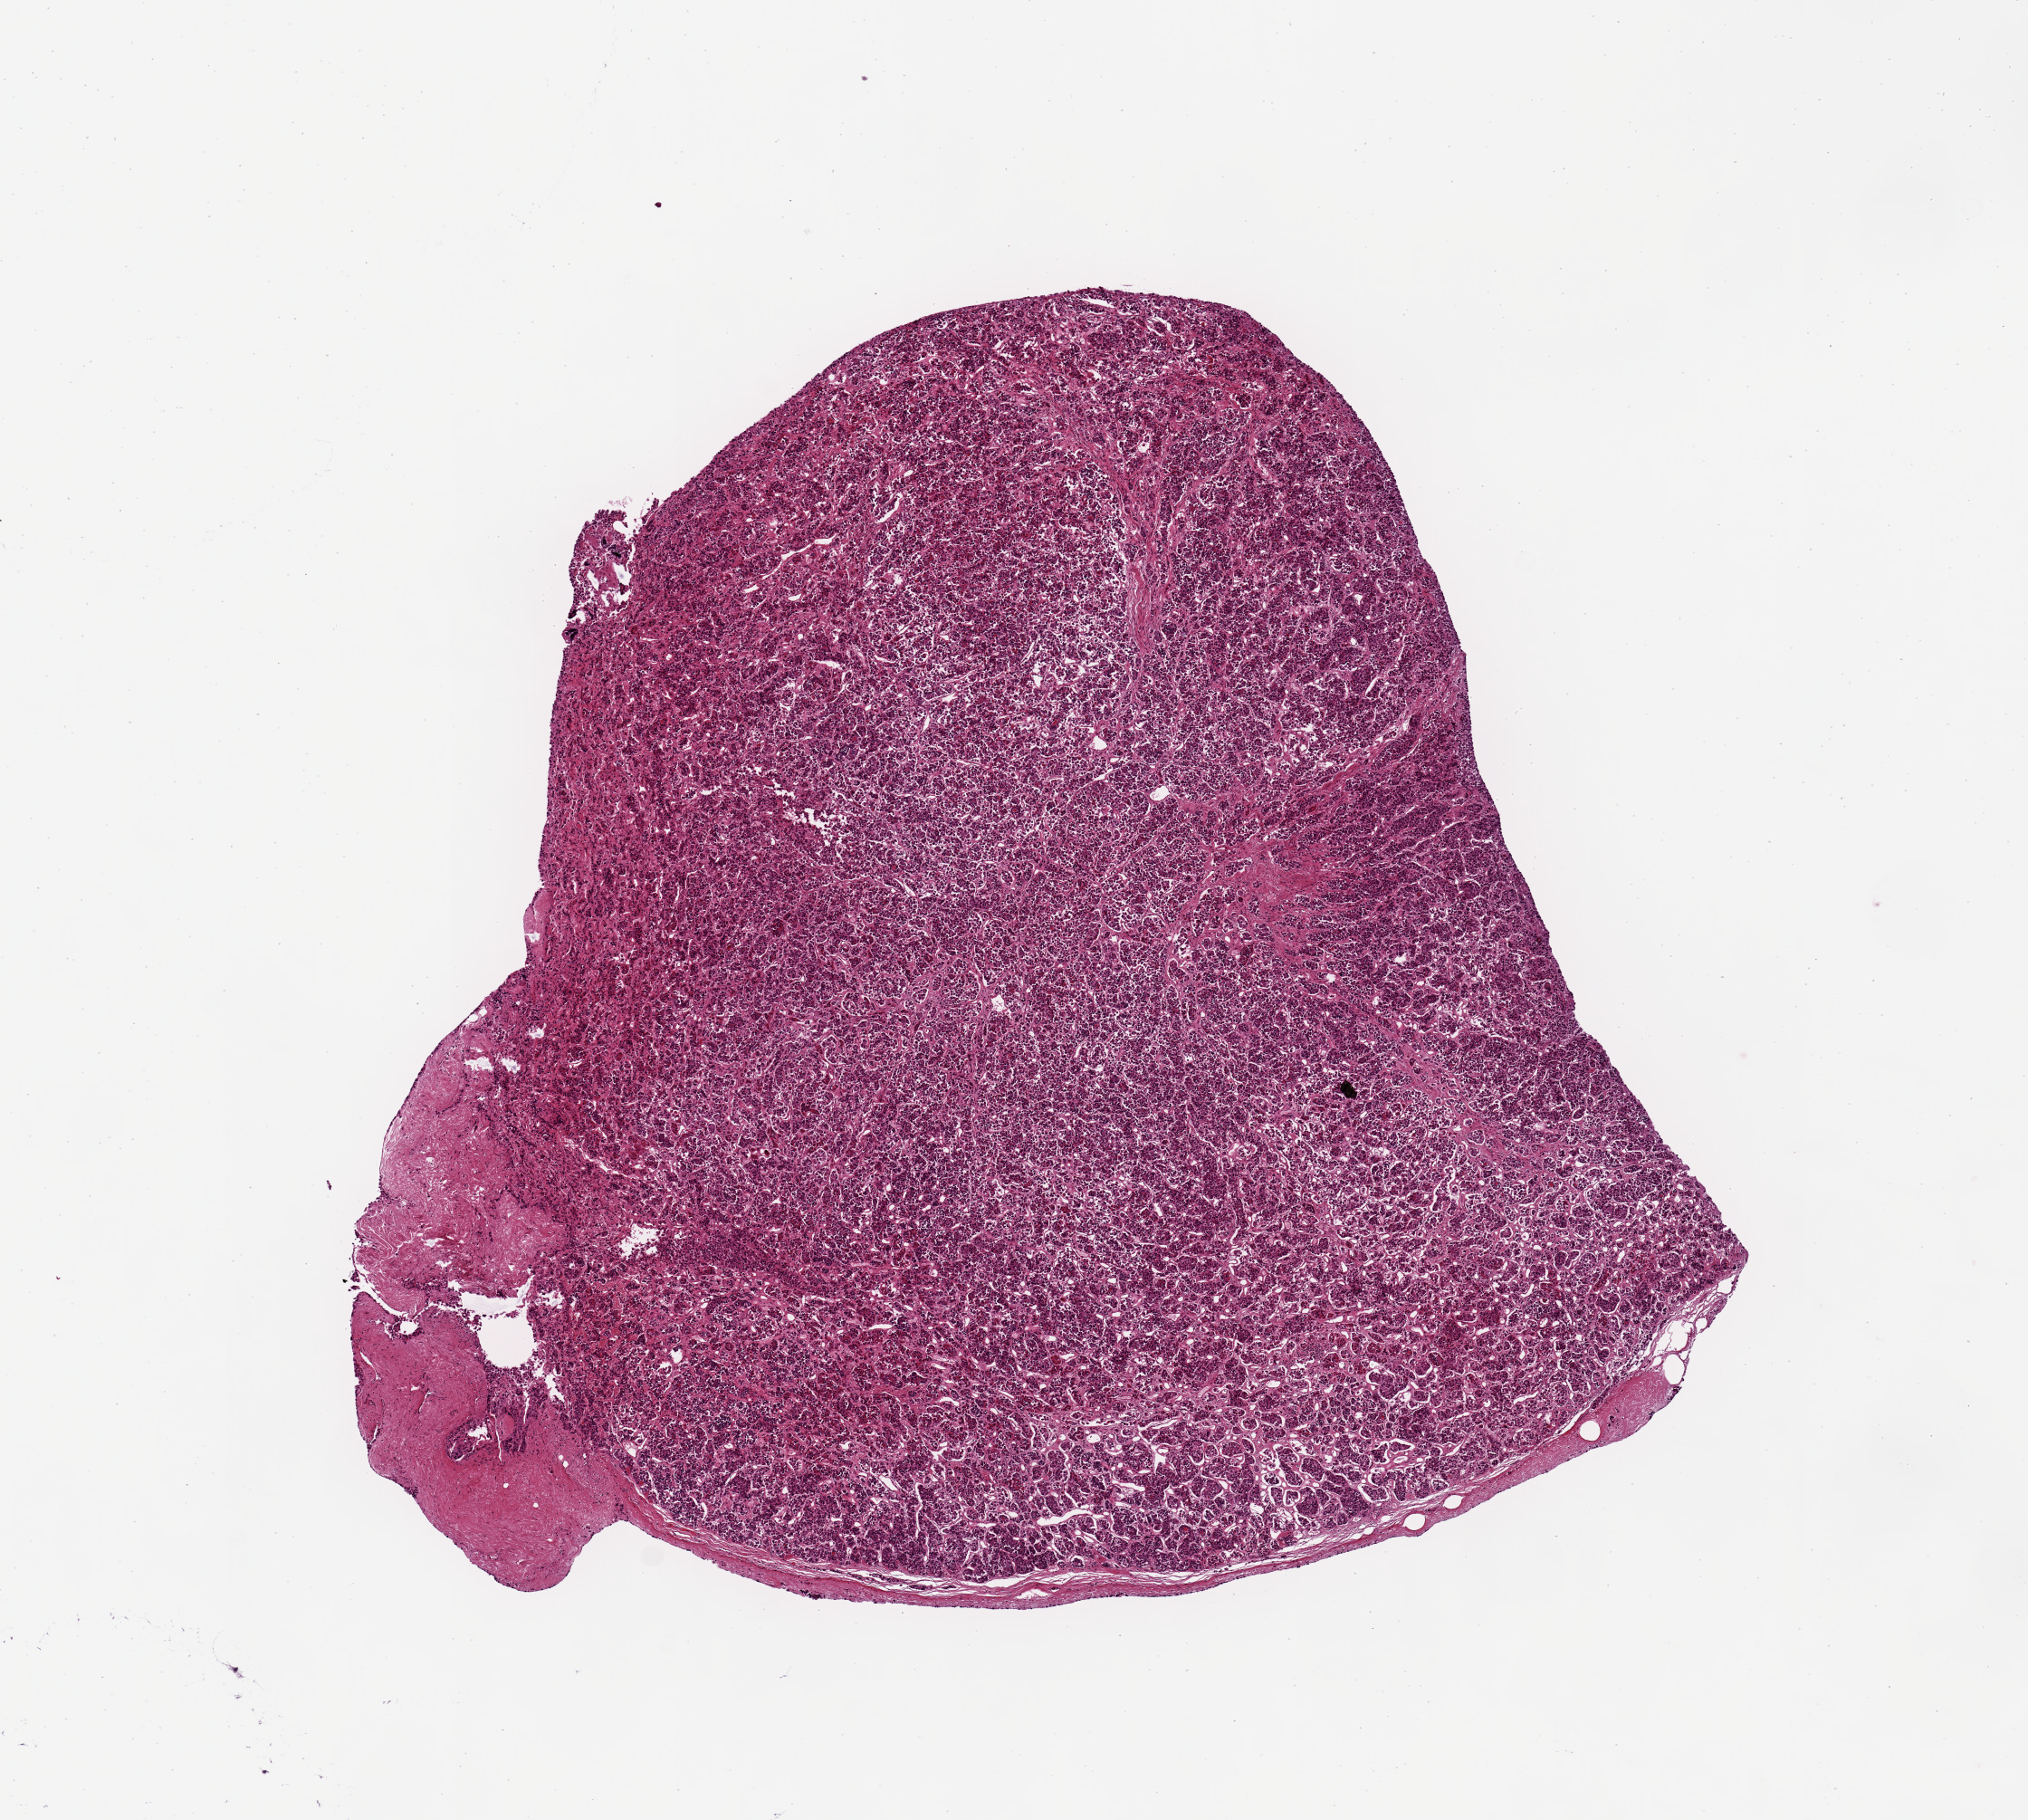
H&E whole-slide image, low-resolution overview of the scanned area, about 8.9 x 7.9 mm. PAXgene-fixed, paraffin-embedded tissue. Section of pituitary (target tissue). Donor tissue sample. Donor sex: male.
Review note (as recorded): 1 piece, 6x5.6 mm.